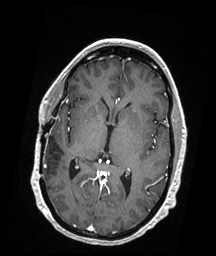
Brain MRI from a brain-tumour surgery series, one axial slice. T1-weighted post-contrast. 1 mm slice thickness. 216 × 256 image matrix, field of view 211 × 250 mm. Case-level facts recorded for this patient, not image findings: histopathology: Demyelinating Lesions (Multiple Sclerosis Plaques); tumour location: Left Occipital.
Outlined on this slice (outlined manually by an expert reader):
- tumour: bounding box (x1, y1, x2, y2) in pixels: (121, 208, 127, 213)